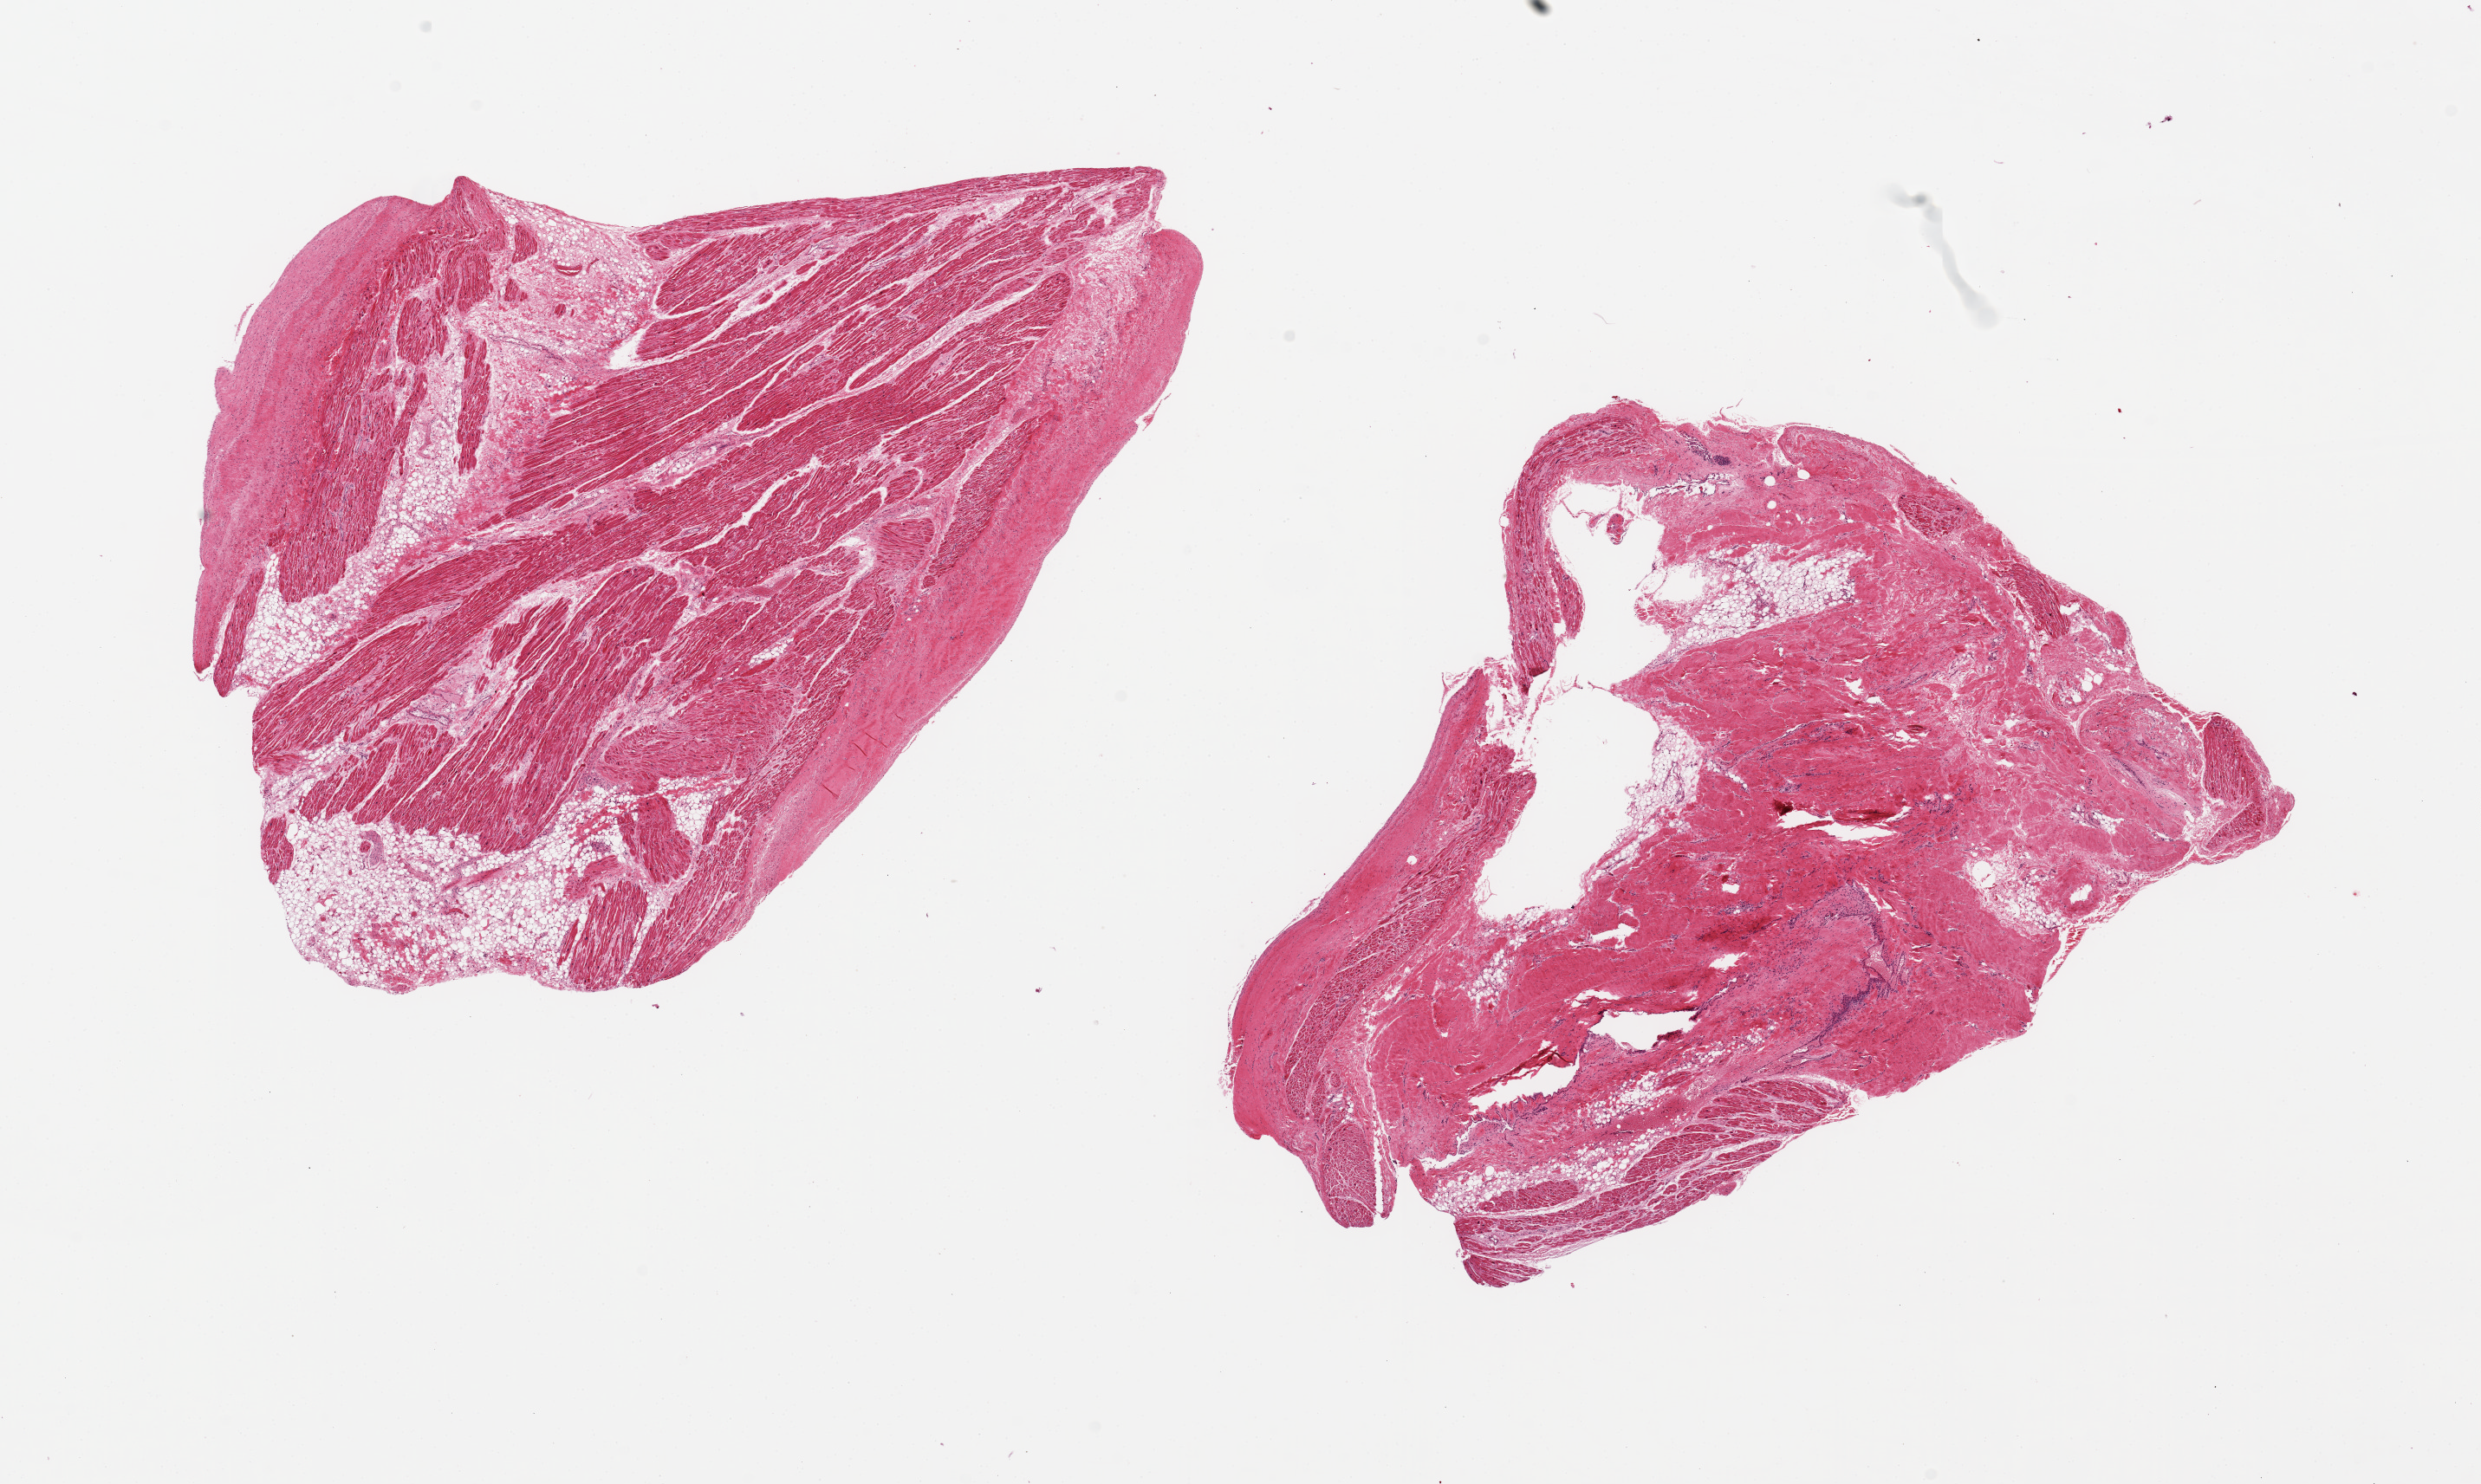
Digitized H&E-stained section, a low-resolution overview of the entire scanned area, about 22.6 x 13.5 mm, PAXgene-fixed, paraffin-embedded tissue, section of auricular appendage (target tissue), tissue donor sample. Donor sex: male.
Review note (as recorded): 2 pieces 10.5x7 & 10x7mm.